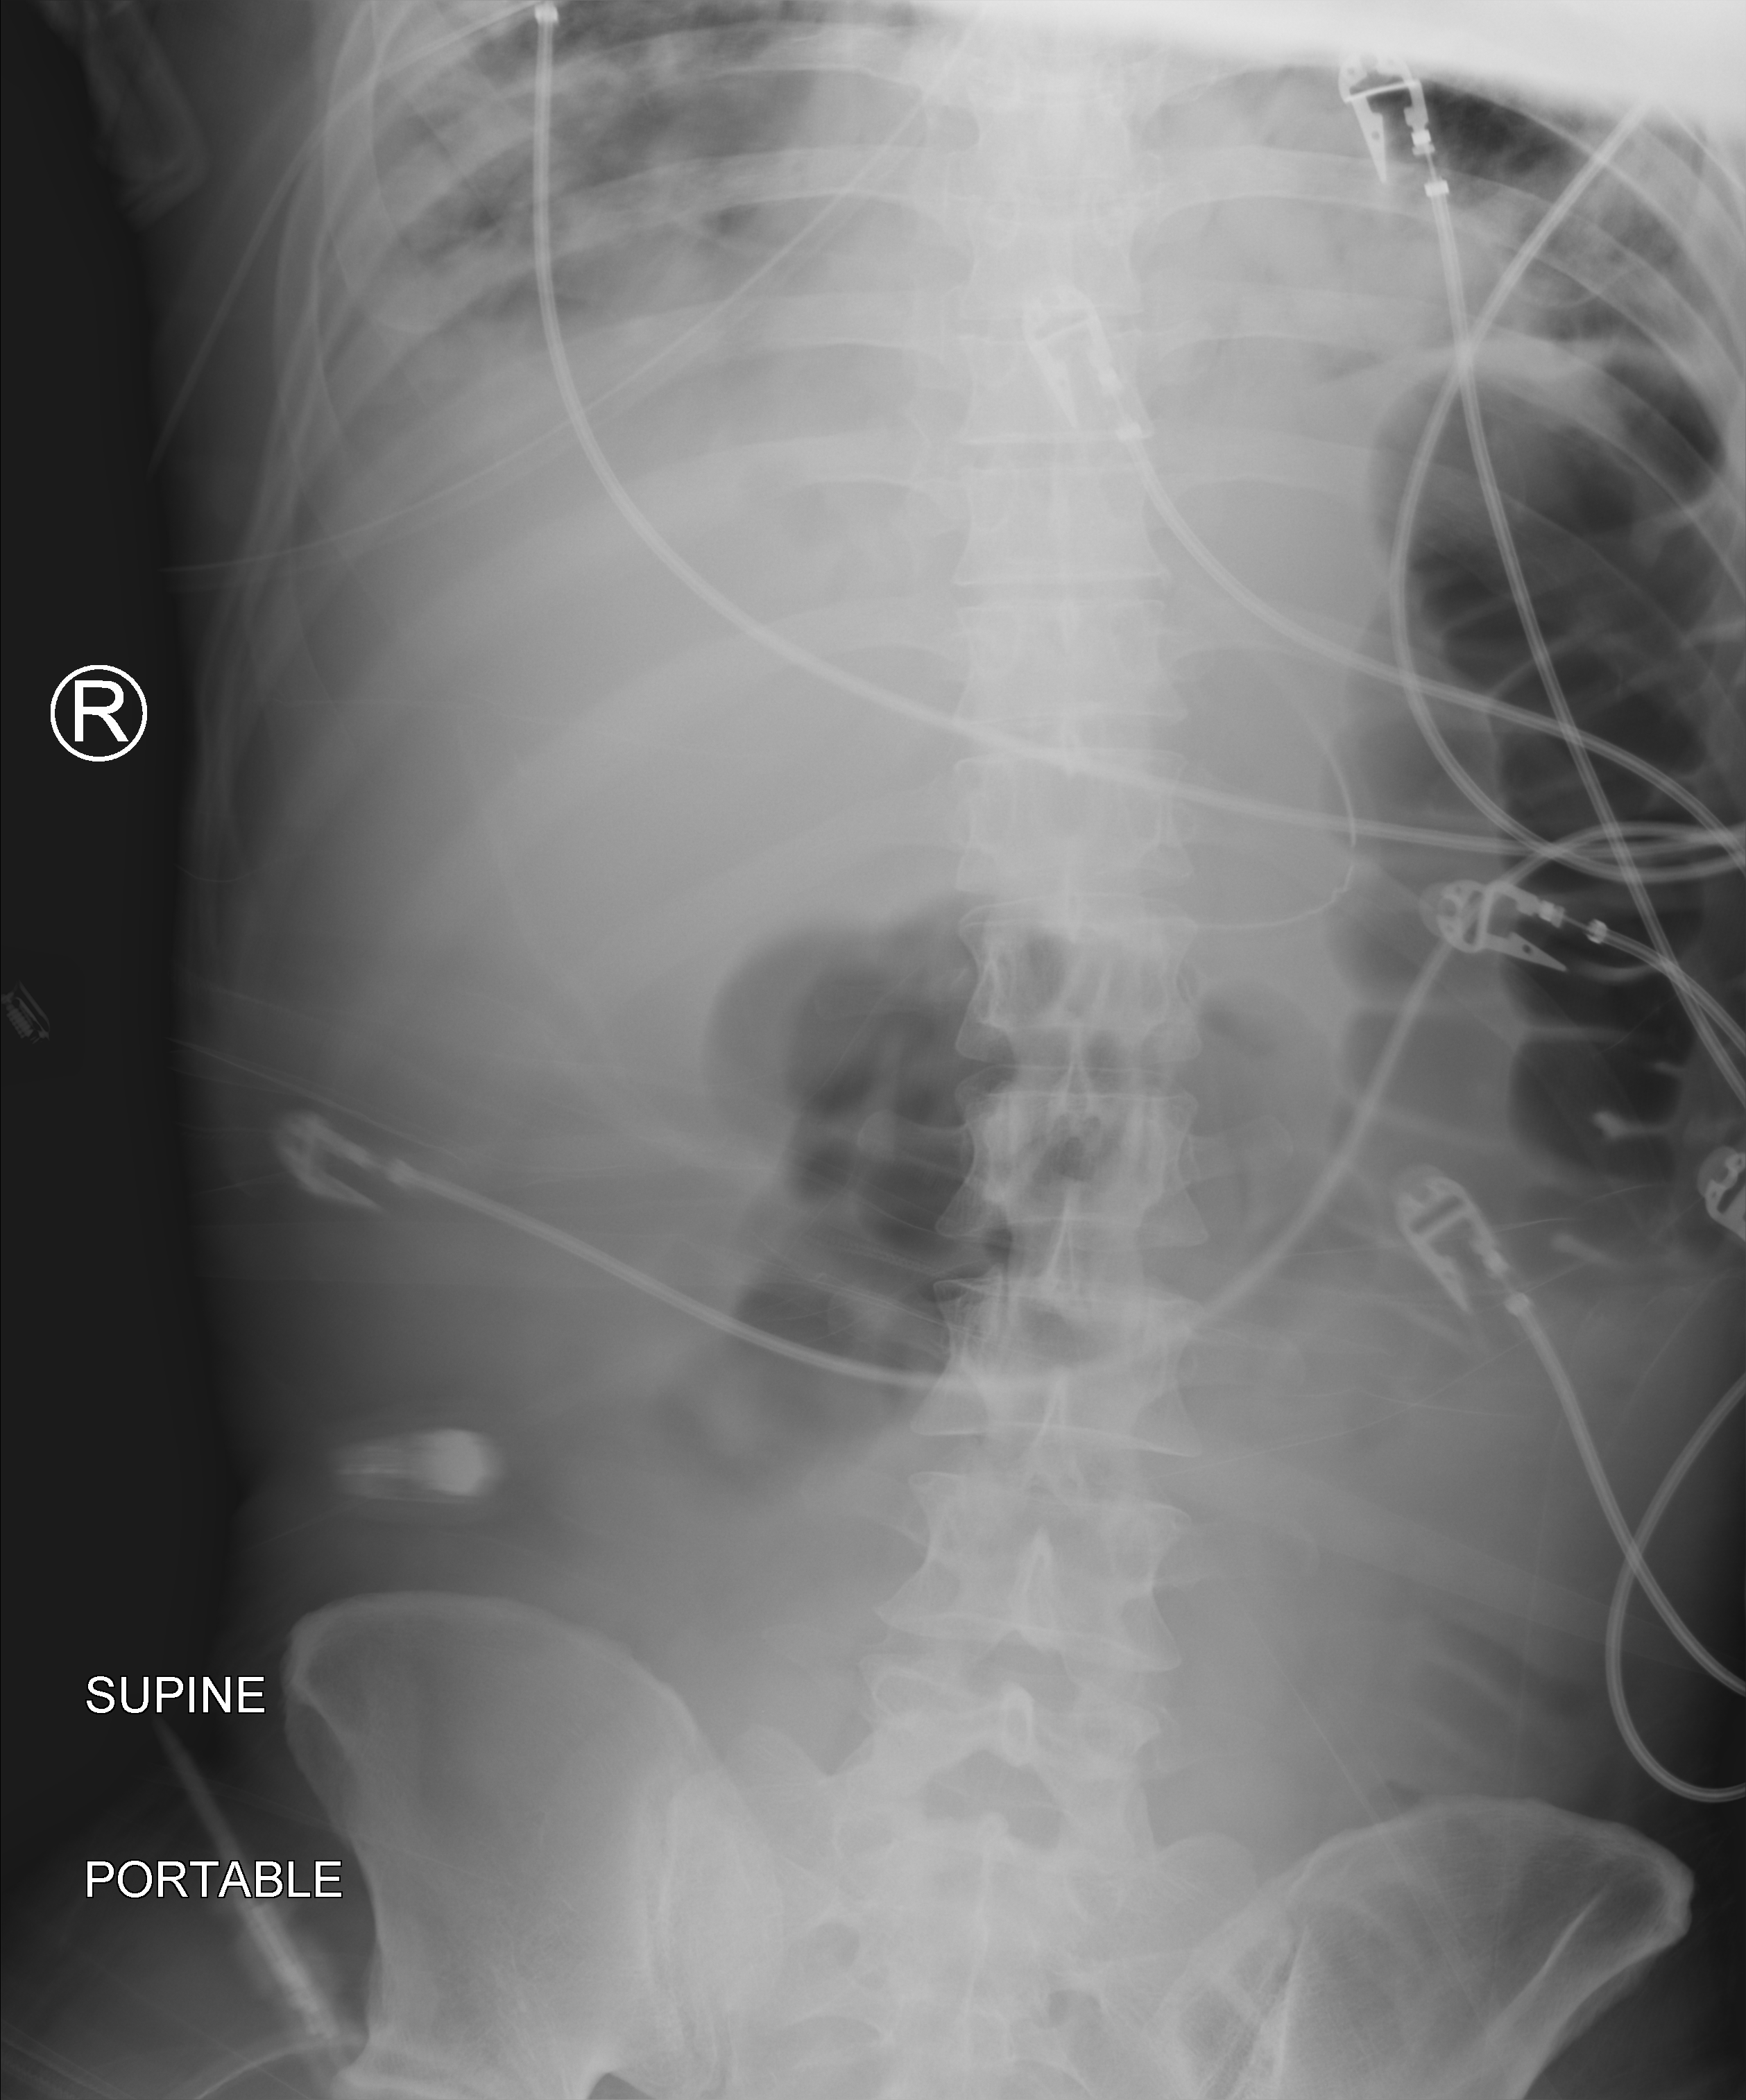
Bedside abdomen radiograph (computed radiography); anteroposterior (AP) projection. Male patient hospitalised with COVID-19, age 18–59 years.
Hospital-stay facts (about this admission, not read from this image; timing relative to this image not recorded): mechanically ventilated during this hospital stay: yes.